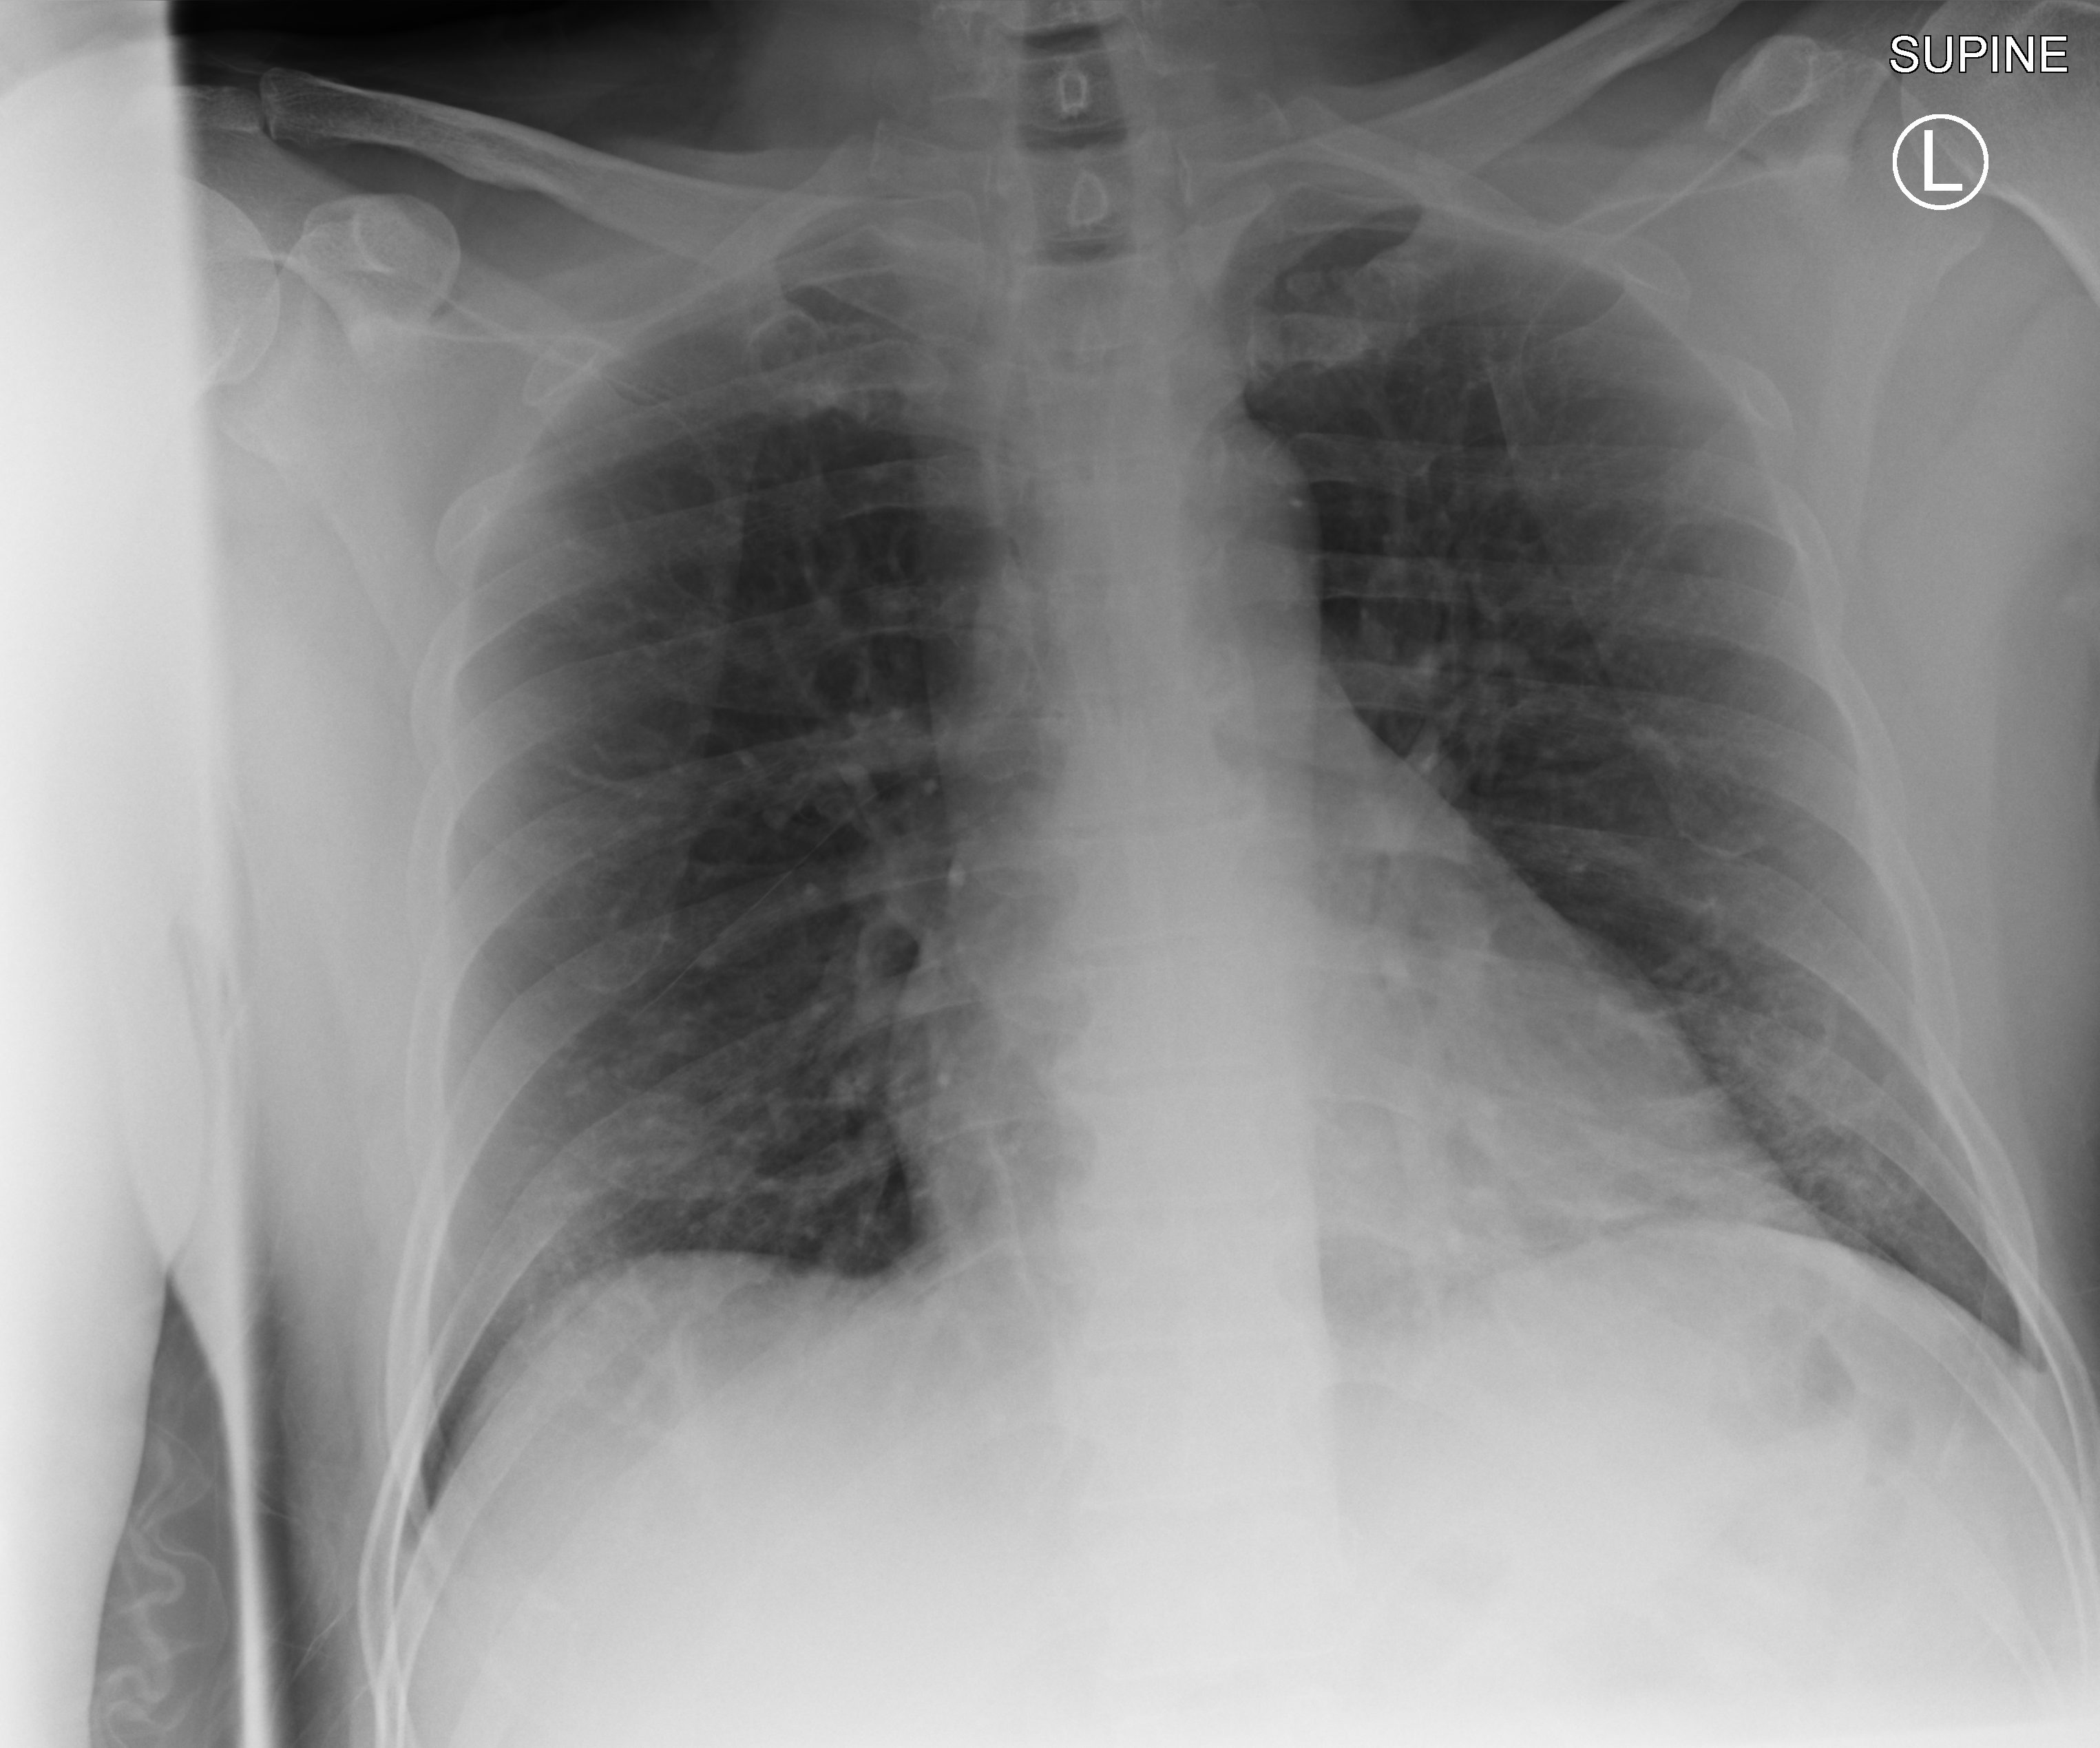
Chest X-ray (portable), anteroposterior (AP) projection. Patient hospitalised with COVID-19; male, aged 18–59 years.
Hospital-stay facts (about this admission, not read from this image; timing relative to this image not recorded):
- mechanically ventilated during this hospital stay: no
- diabetes (admission record): no